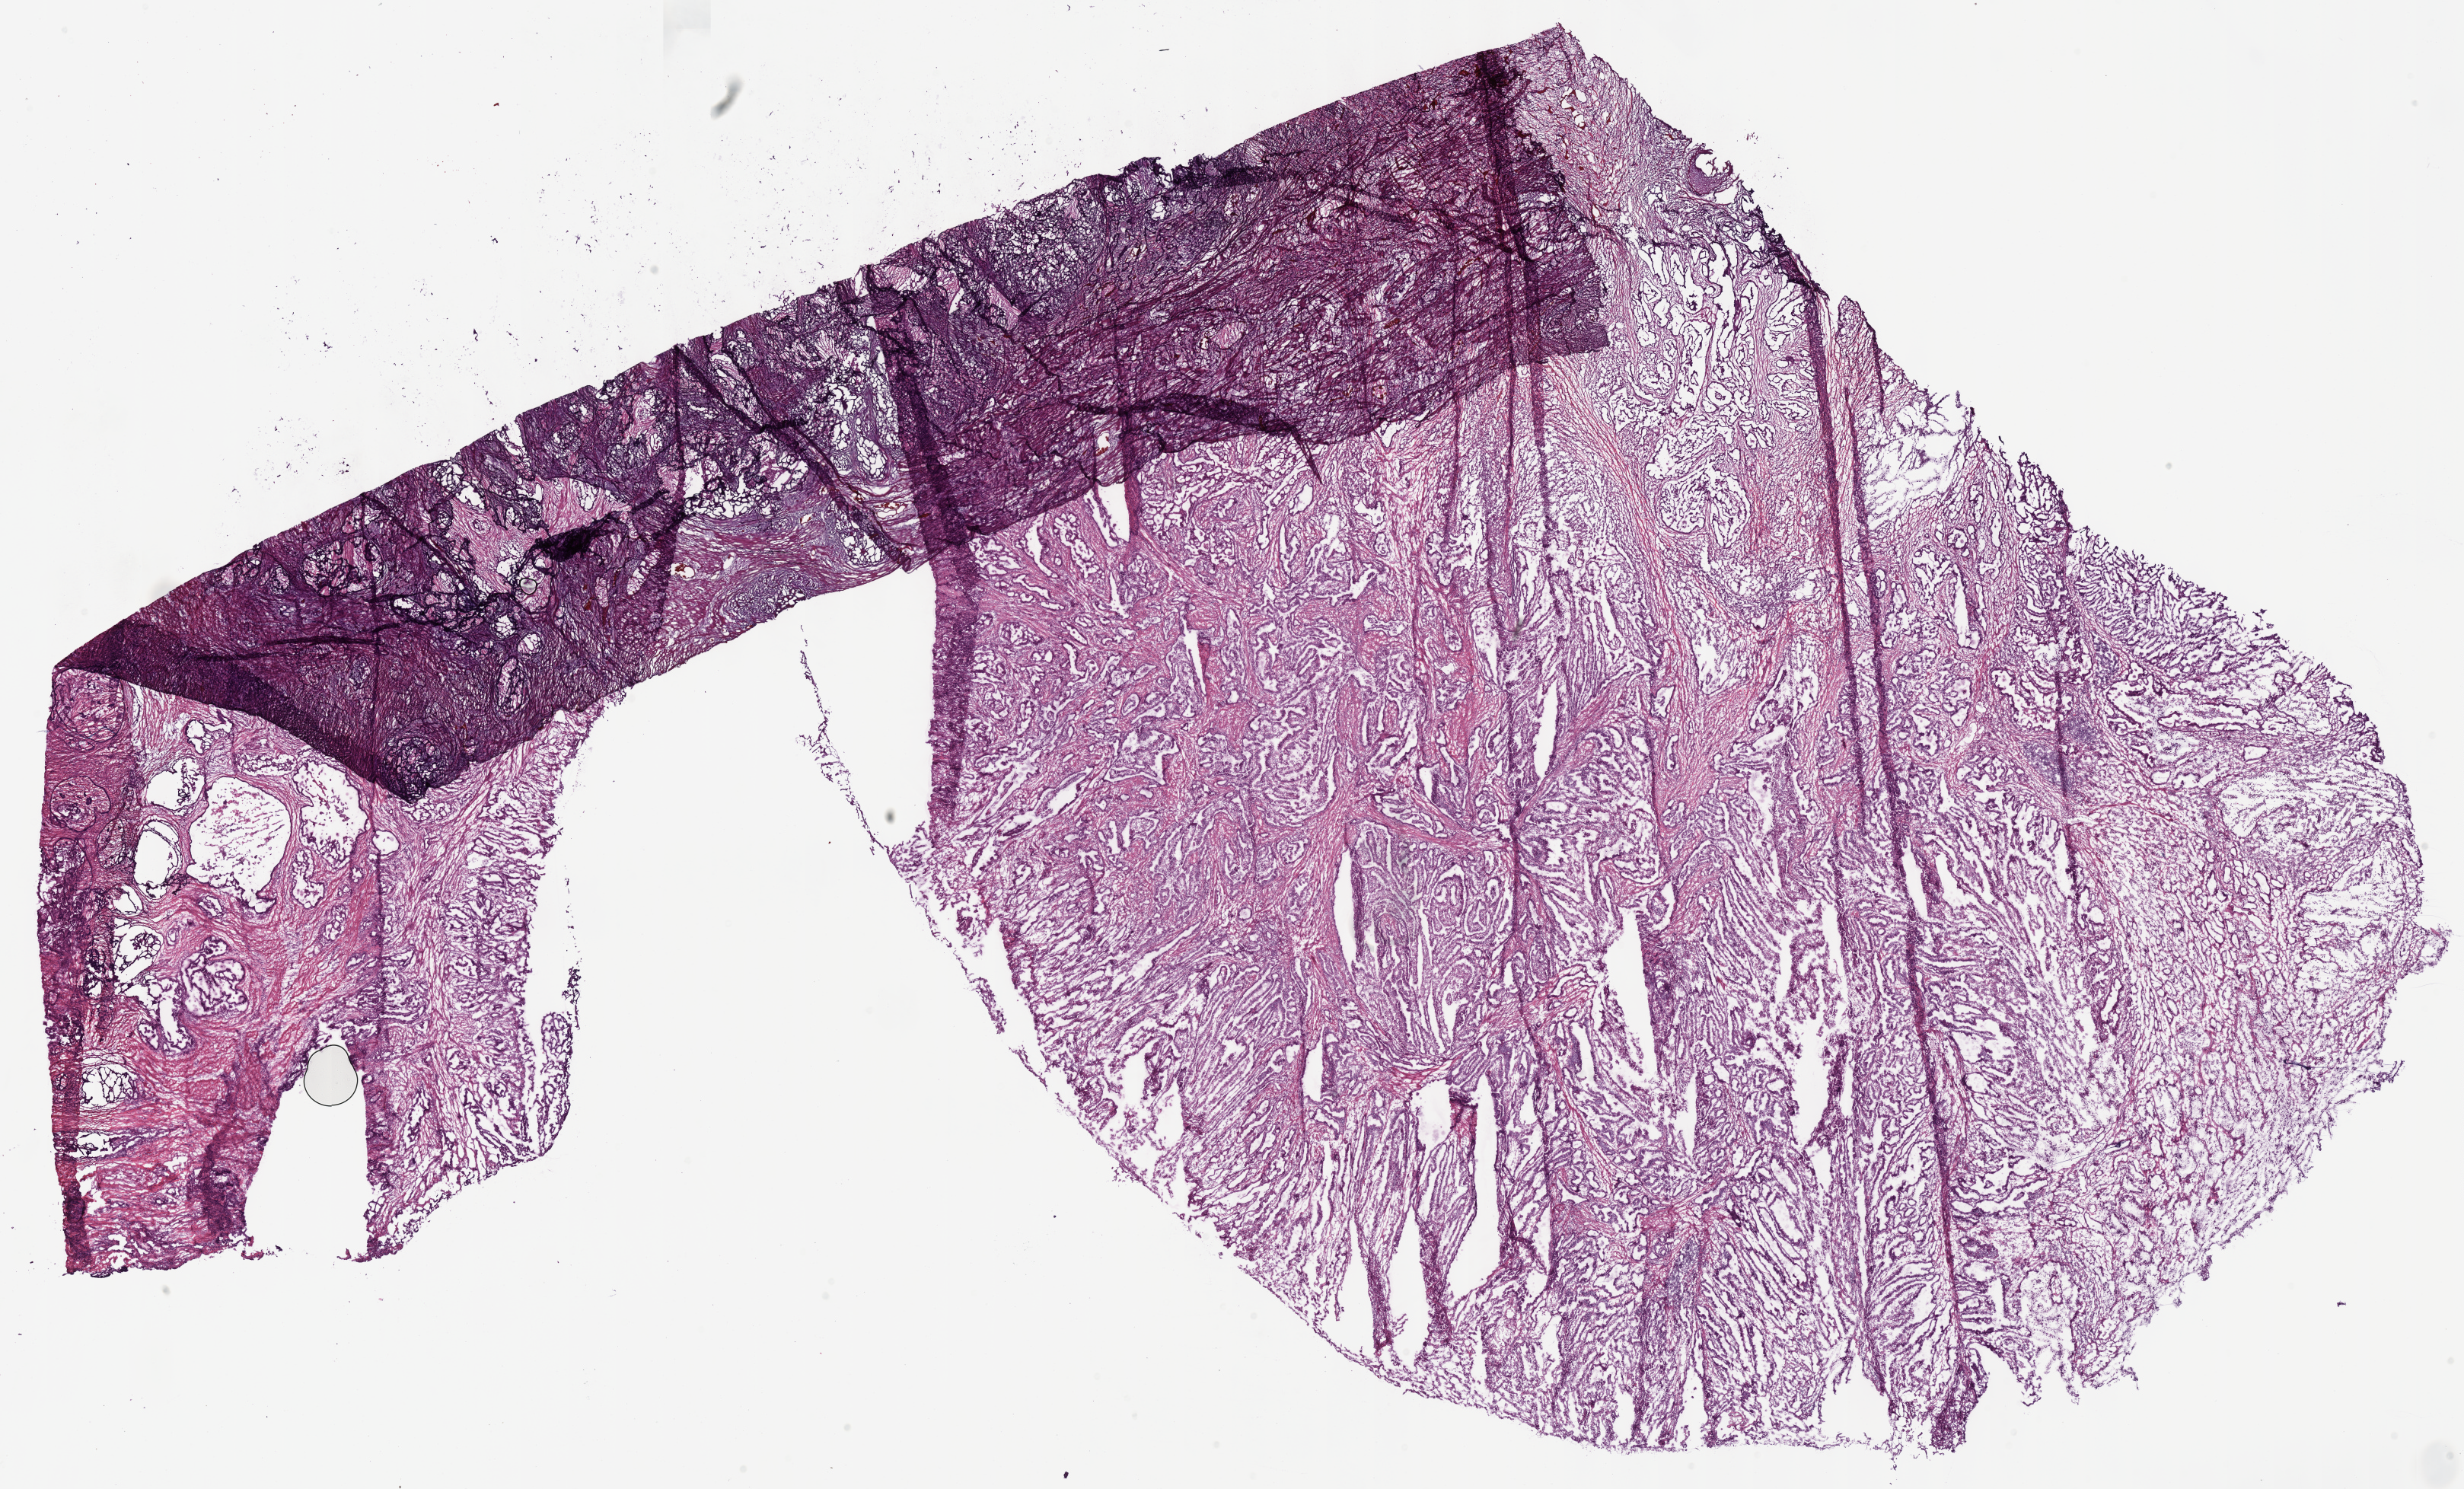
H&E-stained whole-slide image — a low-resolution overview of the entire scanned area, about 25.5 x 15.4 mm (acquisition: 40x scan); frozen section from the bottom of the tissue portion; sample: primary tumour, stomach. Male, age 49 years at initial diagnosis. Histologic grade: G3 (poorly differentiated). Pathologist review of this section (percent, as recorded): tumour cells 80%, tumour nuclei 85%, normal cells 0%, stromal cells 15%, necrosis 5%.
Histologic diagnosis: Adenocarcinoma, intestinal type (gastric antrum). Lymph nodes positive (case pathology): 0 of 5 examined. AJCC pathologic stage: II.